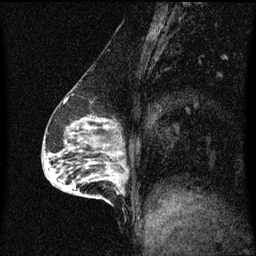
Breast MRI (dynamic contrast-enhanced), one sagittal slice; slice 26 of 60 in the series (ordered by position); dynamic contrast-enhanced series, image 2 of 3 at this slice position (ordered by acquisition); 1.5 T; TE 4.2 ms, TR 8.4 ms; 2 mm slice thickness; 256 × 256 image matrix, field of view 200 × 200 mm. Patient: female, 64 years.
Annotated regions visible in this slice (semi-automatically segmented with operator editing):
- analysis volume of interest (the breast-tissue region the enhancement analysis was run in; not a lesion): box from (x=90, y=164) to (x=129, y=203) px
- tumour enhancement mask (voxels above the 70 % enhancement threshold inside the analysis volume of interest): (x=92, y=170)–(x=129, y=193)